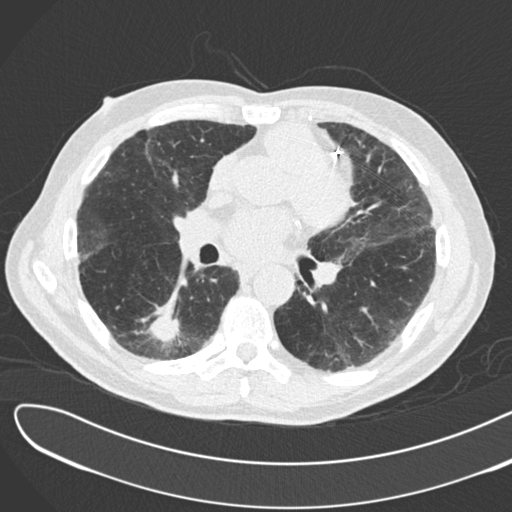
Low-dose screening chest CT, one axial slice. Slice 88 of 183 in the series (ordered by position). Reconstruction kernel B30f. 120 kVp. Lung window (W 1500 / L -600 HU). 2 mm slice thickness. 512 × 512 image matrix.
Structures marked on this image (manually delineated by an expert):
- lesion 1 (tumor, lower lobe of right lung): bounding box (x1, y1, x2, y2) in pixels: (148, 301, 182, 344)